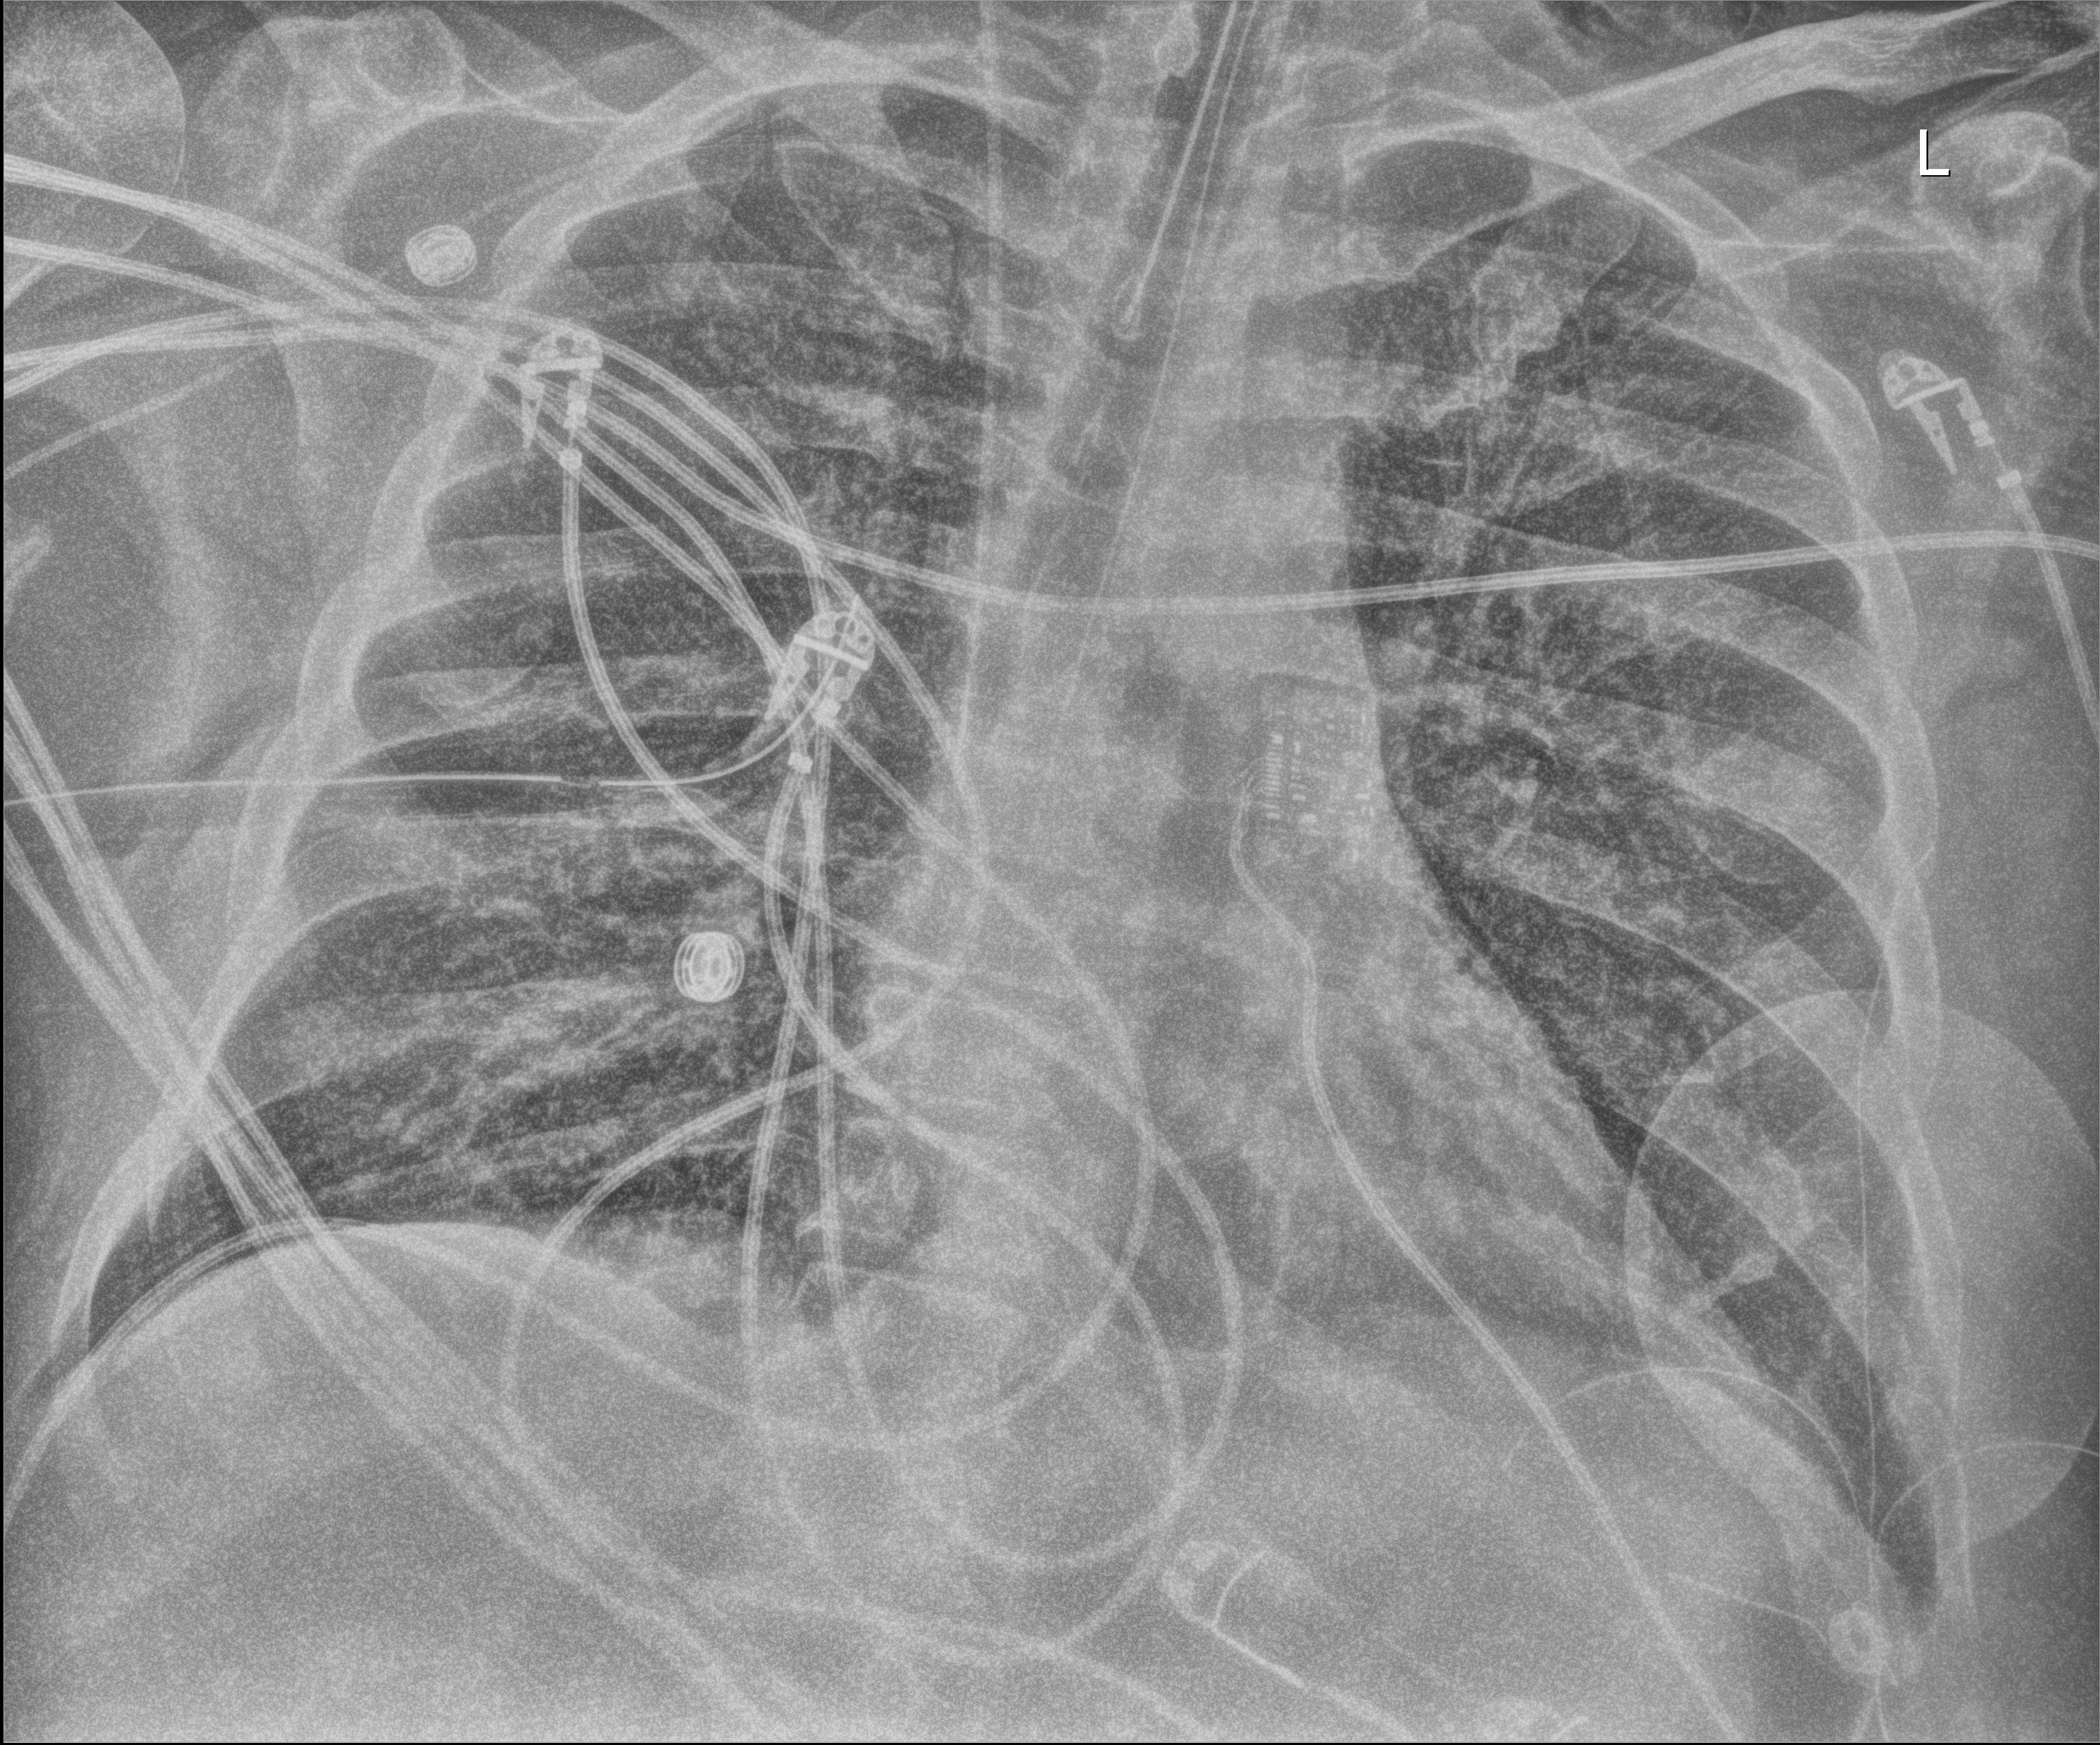
Portable chest radiograph. Adult patient hospitalised with COVID-19, age 18–59 years.
Hospital-stay facts (about this admission, not read from this image; timing relative to this image not recorded):
- admitted to intensive care during this hospital stay: yes